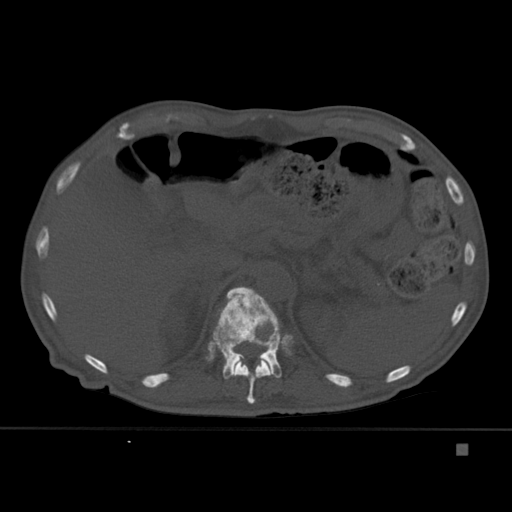
CT including the spine, one axial slice. Slice 207 of 451 in the series (ordered by position). Bone window (W 1800 / L 400 HU). 1.5 mm slice thickness. 512 × 512 image matrix, field of view 378 × 378 mm. Male patient, age 75 years. From the clinical record (not read from this slice): primary cancer: prostate.
Structures marked on this image (semi-automatic segmentation, software-assisted and operator-edited):
- T11 vertebra: box from (x=234, y=358) to (x=272, y=404) px
- T12 vertebra: (x=212, y=287)–(x=282, y=379)